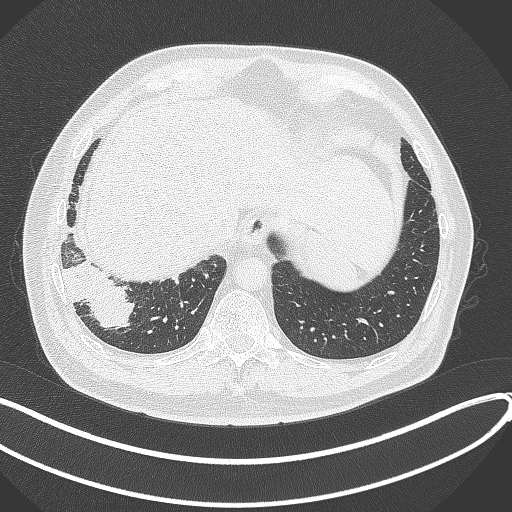
Chest CT, one axial slice. Reconstruction kernel B70f. 120 kVp. Lung window (W 1500 / L -600 HU). 512 × 512 image matrix, field of view 400 × 400 mm. Male patient, age 59 years.
Annotated regions visible in this slice (rectangle marked by the reading radiologist):
- lung tumour (recorded histology: adenocarcinoma): bounding box [x1, y1, x2, y2] px = [62, 258, 136, 331]